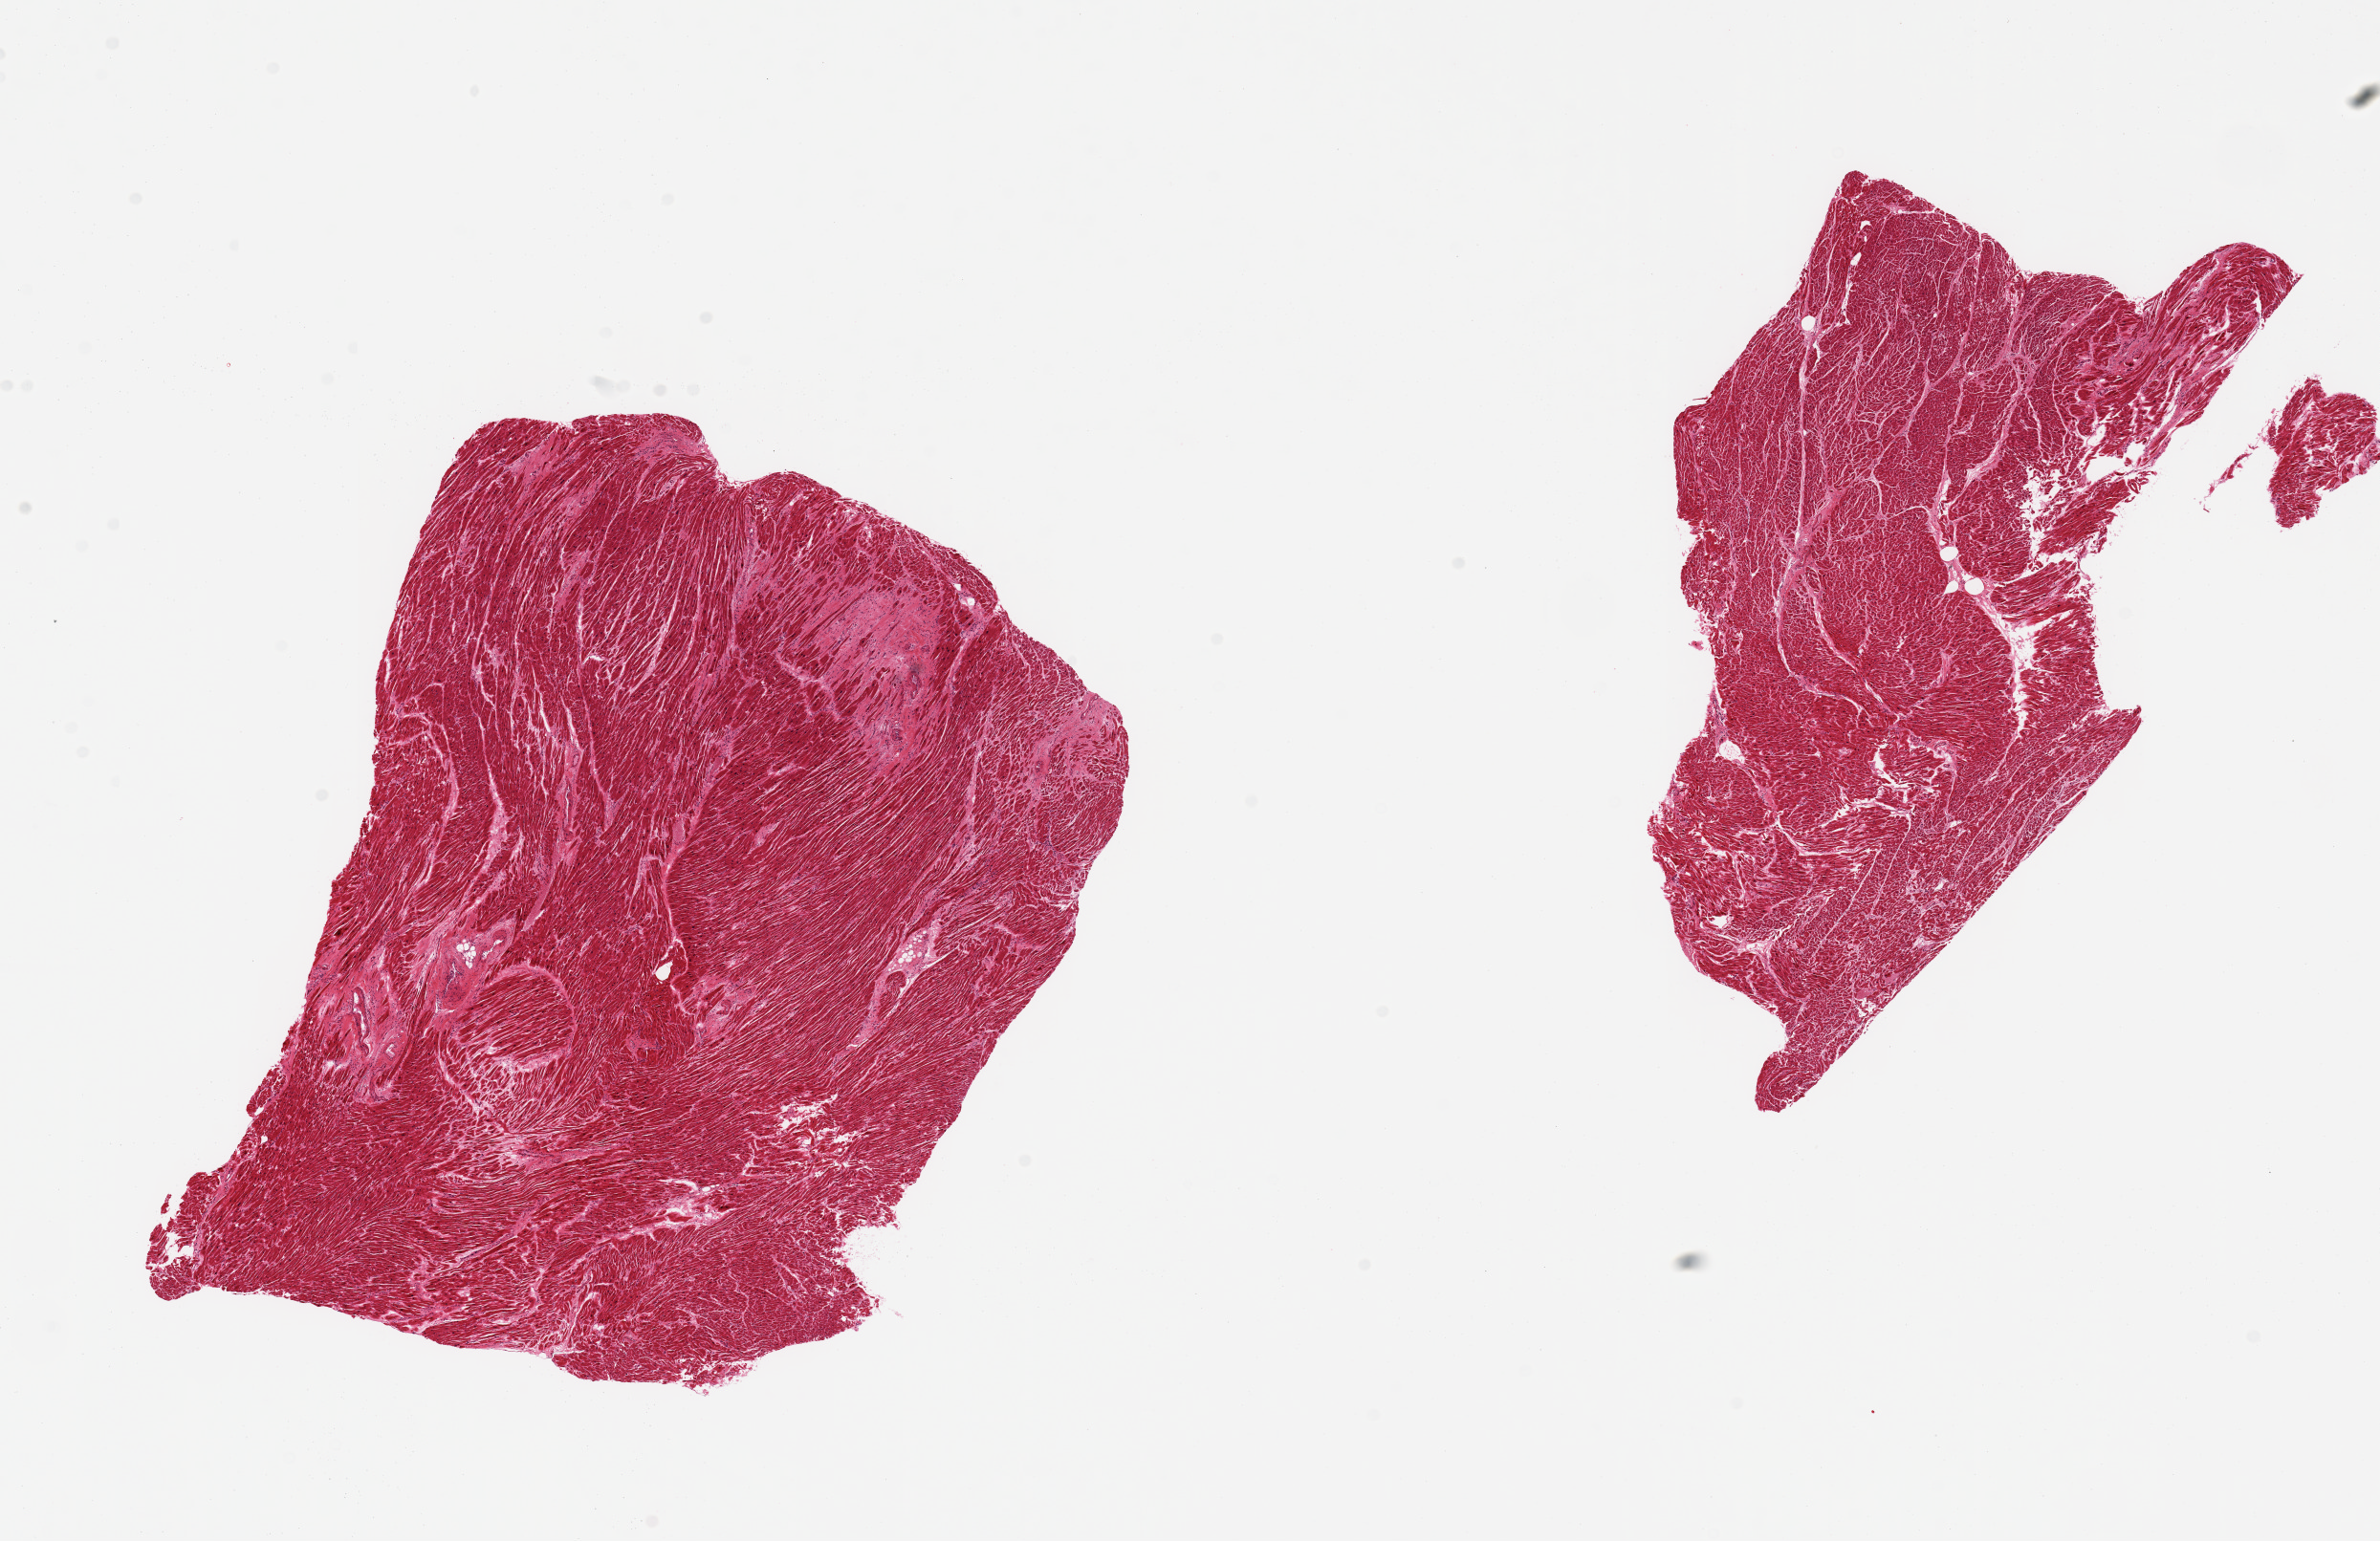
Whole-slide image, hematoxylin and eosin (H&E) stain — a low-resolution overview of the entire scanned area, about 19.7 x 12.8 mm; PAXgene-fixed, paraffin-embedded tissue; target tissue: heart; tissue donor sample. Female donor.
Pathologist's review note for this sample: 2 pieces; patchy fibrosis (old infarcts); hypertrophic fibers.